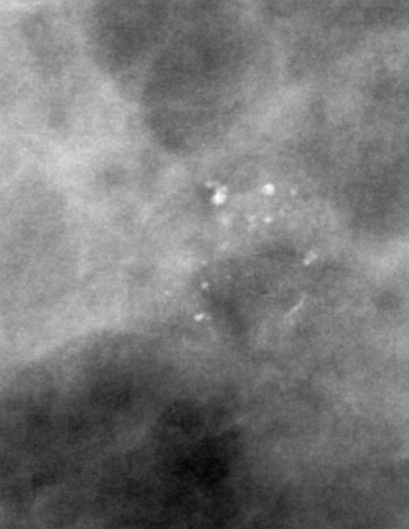
Cropped region of a digitized screen-film mammogram centred on a radiologist-marked abnormality, left breast, MLO view, BI-RADS breast density category 4 (scale 1–4).
Marked abnormality: calcifications, morphology pleomorphic, distribution clustered; BI-RADS assessment category 4; subtlety rating 4 on a 1 (subtle) to 5 (obvious) scale; pathology (as recorded): benign.